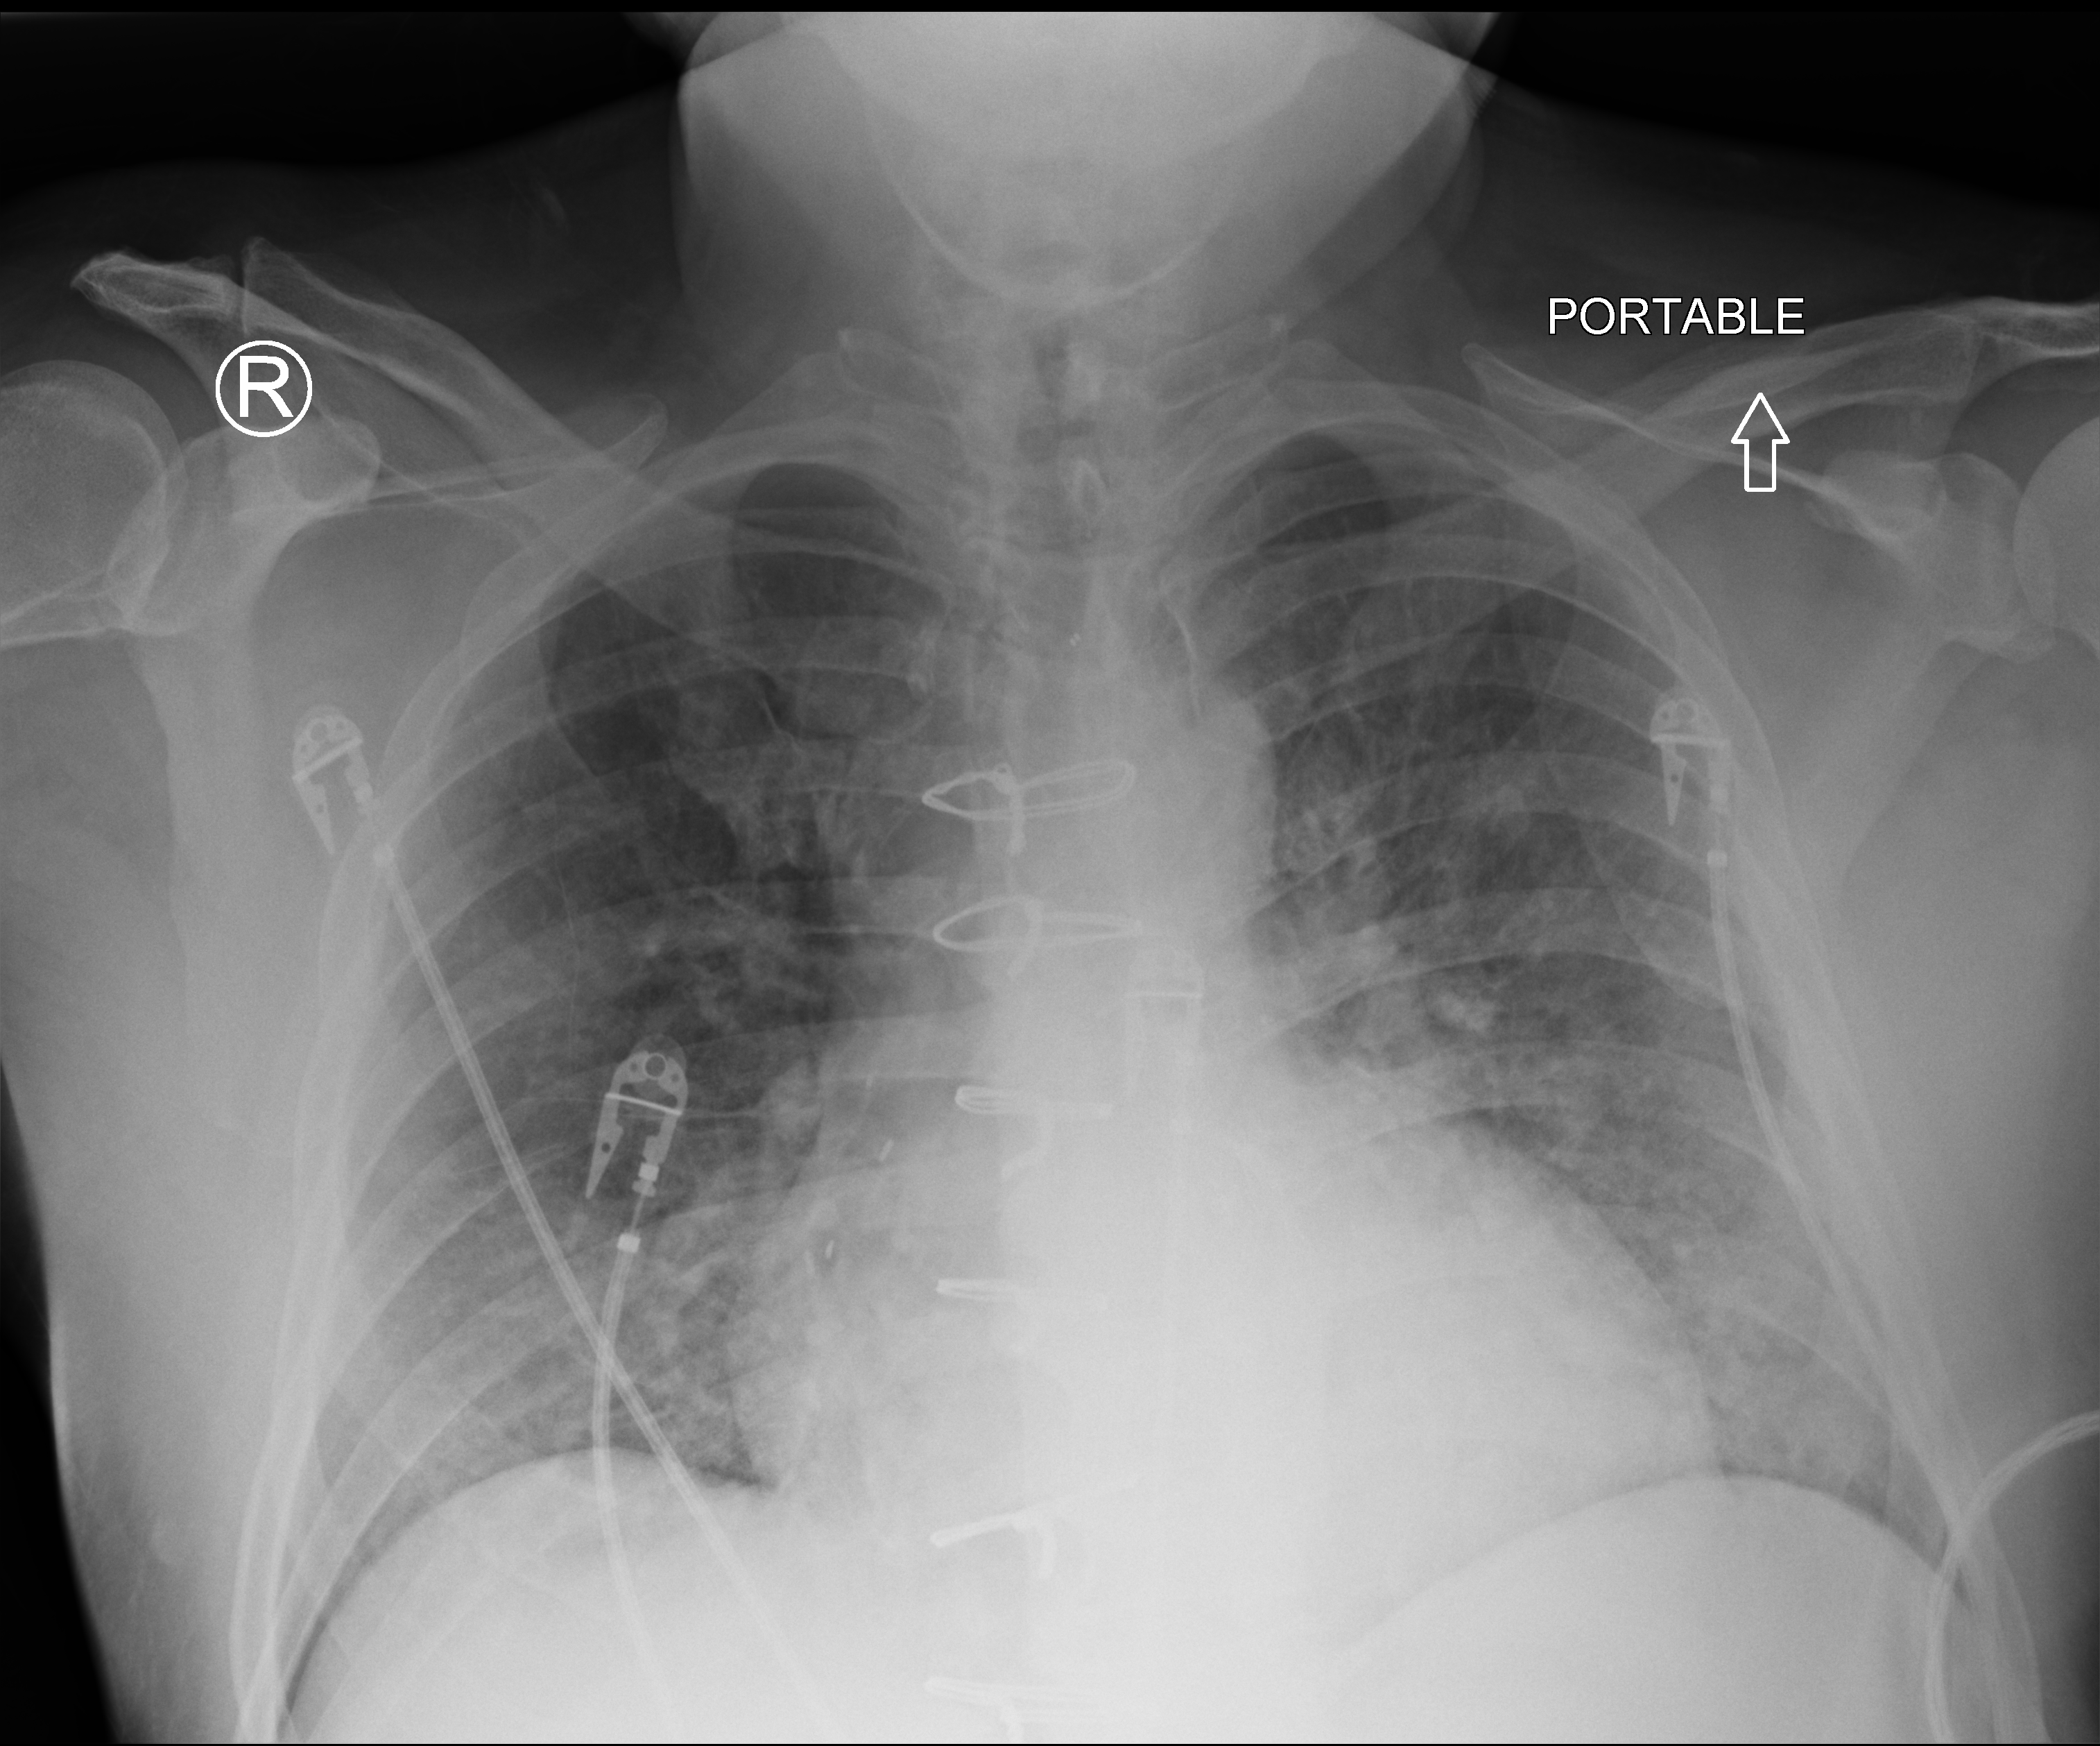
Portable chest radiograph; anteroposterior (AP) projection. Adult patient hospitalised with COVID-19, age 18–59 years.
From the hospital-stay record, not from the radiograph (when in the stay this image was taken is not recorded): other chronic lung disease (admission record): no.